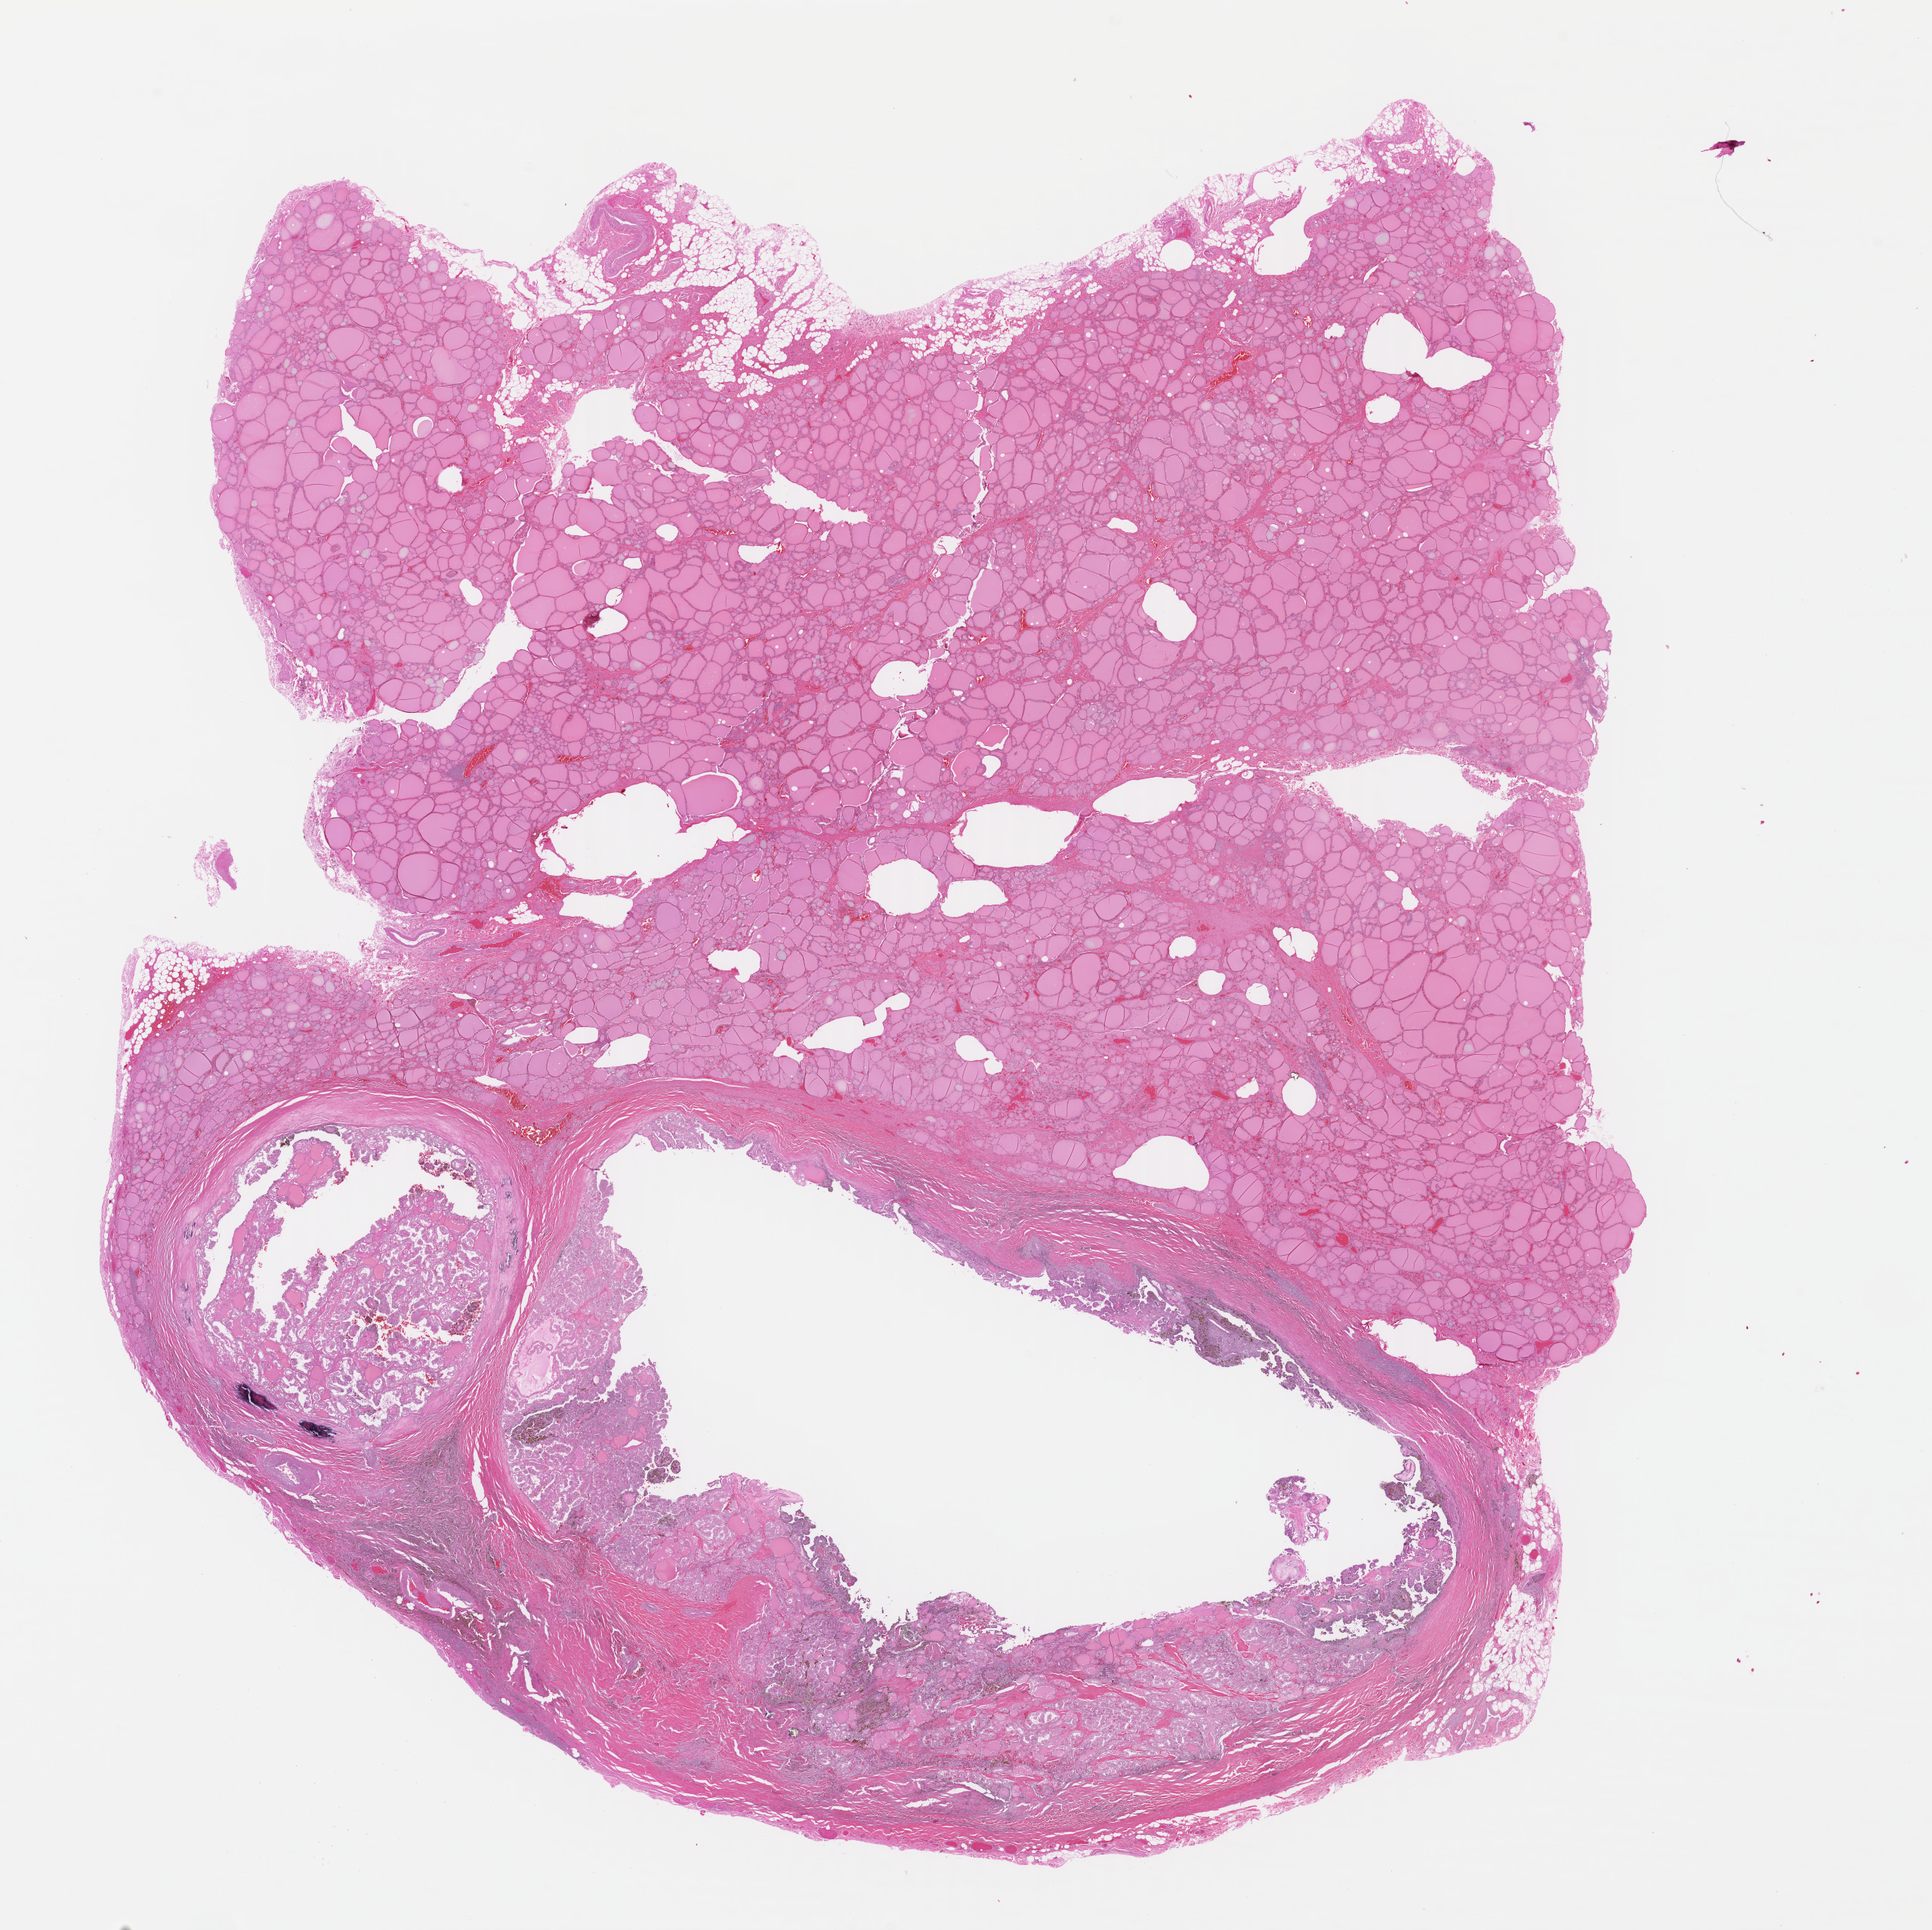
H&E whole-slide image — whole scanned area (about 20.1 x 20.1 mm, from a 40x scan) shown as a low-resolution overview, formalin-fixed paraffin-embedded (FFPE) diagnostic section, thyroid, primary tumour sample. Patient: male, age at initial diagnosis 68 years.
Diagnosis: Papillary adenocarcinoma, NOS (thyroid gland).